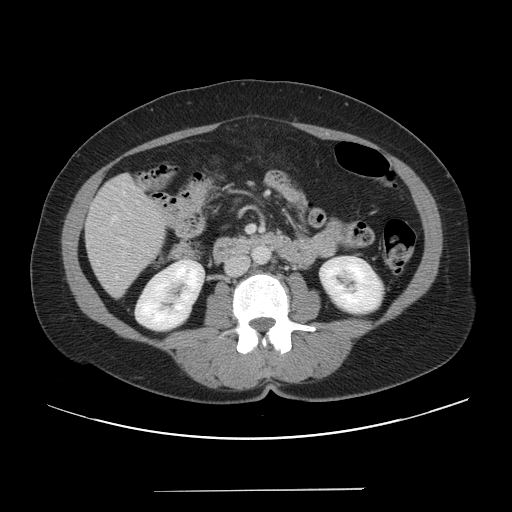
Contrast-enhanced abdominal CT, one axial slice. Slice 12 of 56 in the series (ordered by position). 120 kVp. Intravenous contrast given. Soft-tissue window (W 400 / L 40 HU). 5 mm slice thickness. 512 × 512 image matrix, field of view 419 × 419 mm. Female patient, age 54 years. From the clinical record (not read from this slice): diagnosis: colorectal cancer liver metastases, imaged before liver resection; multiple liver metastases: yes; largest metastasis: 3.2 cm; disease in both lobes: yes.
Annotated regions visible in this slice (outlined manually by an expert reader):
- liver: box from (x=87, y=174) to (x=167, y=297) px
- portal vein (with intrahepatic branches): (x=249, y=226)–(x=254, y=232)